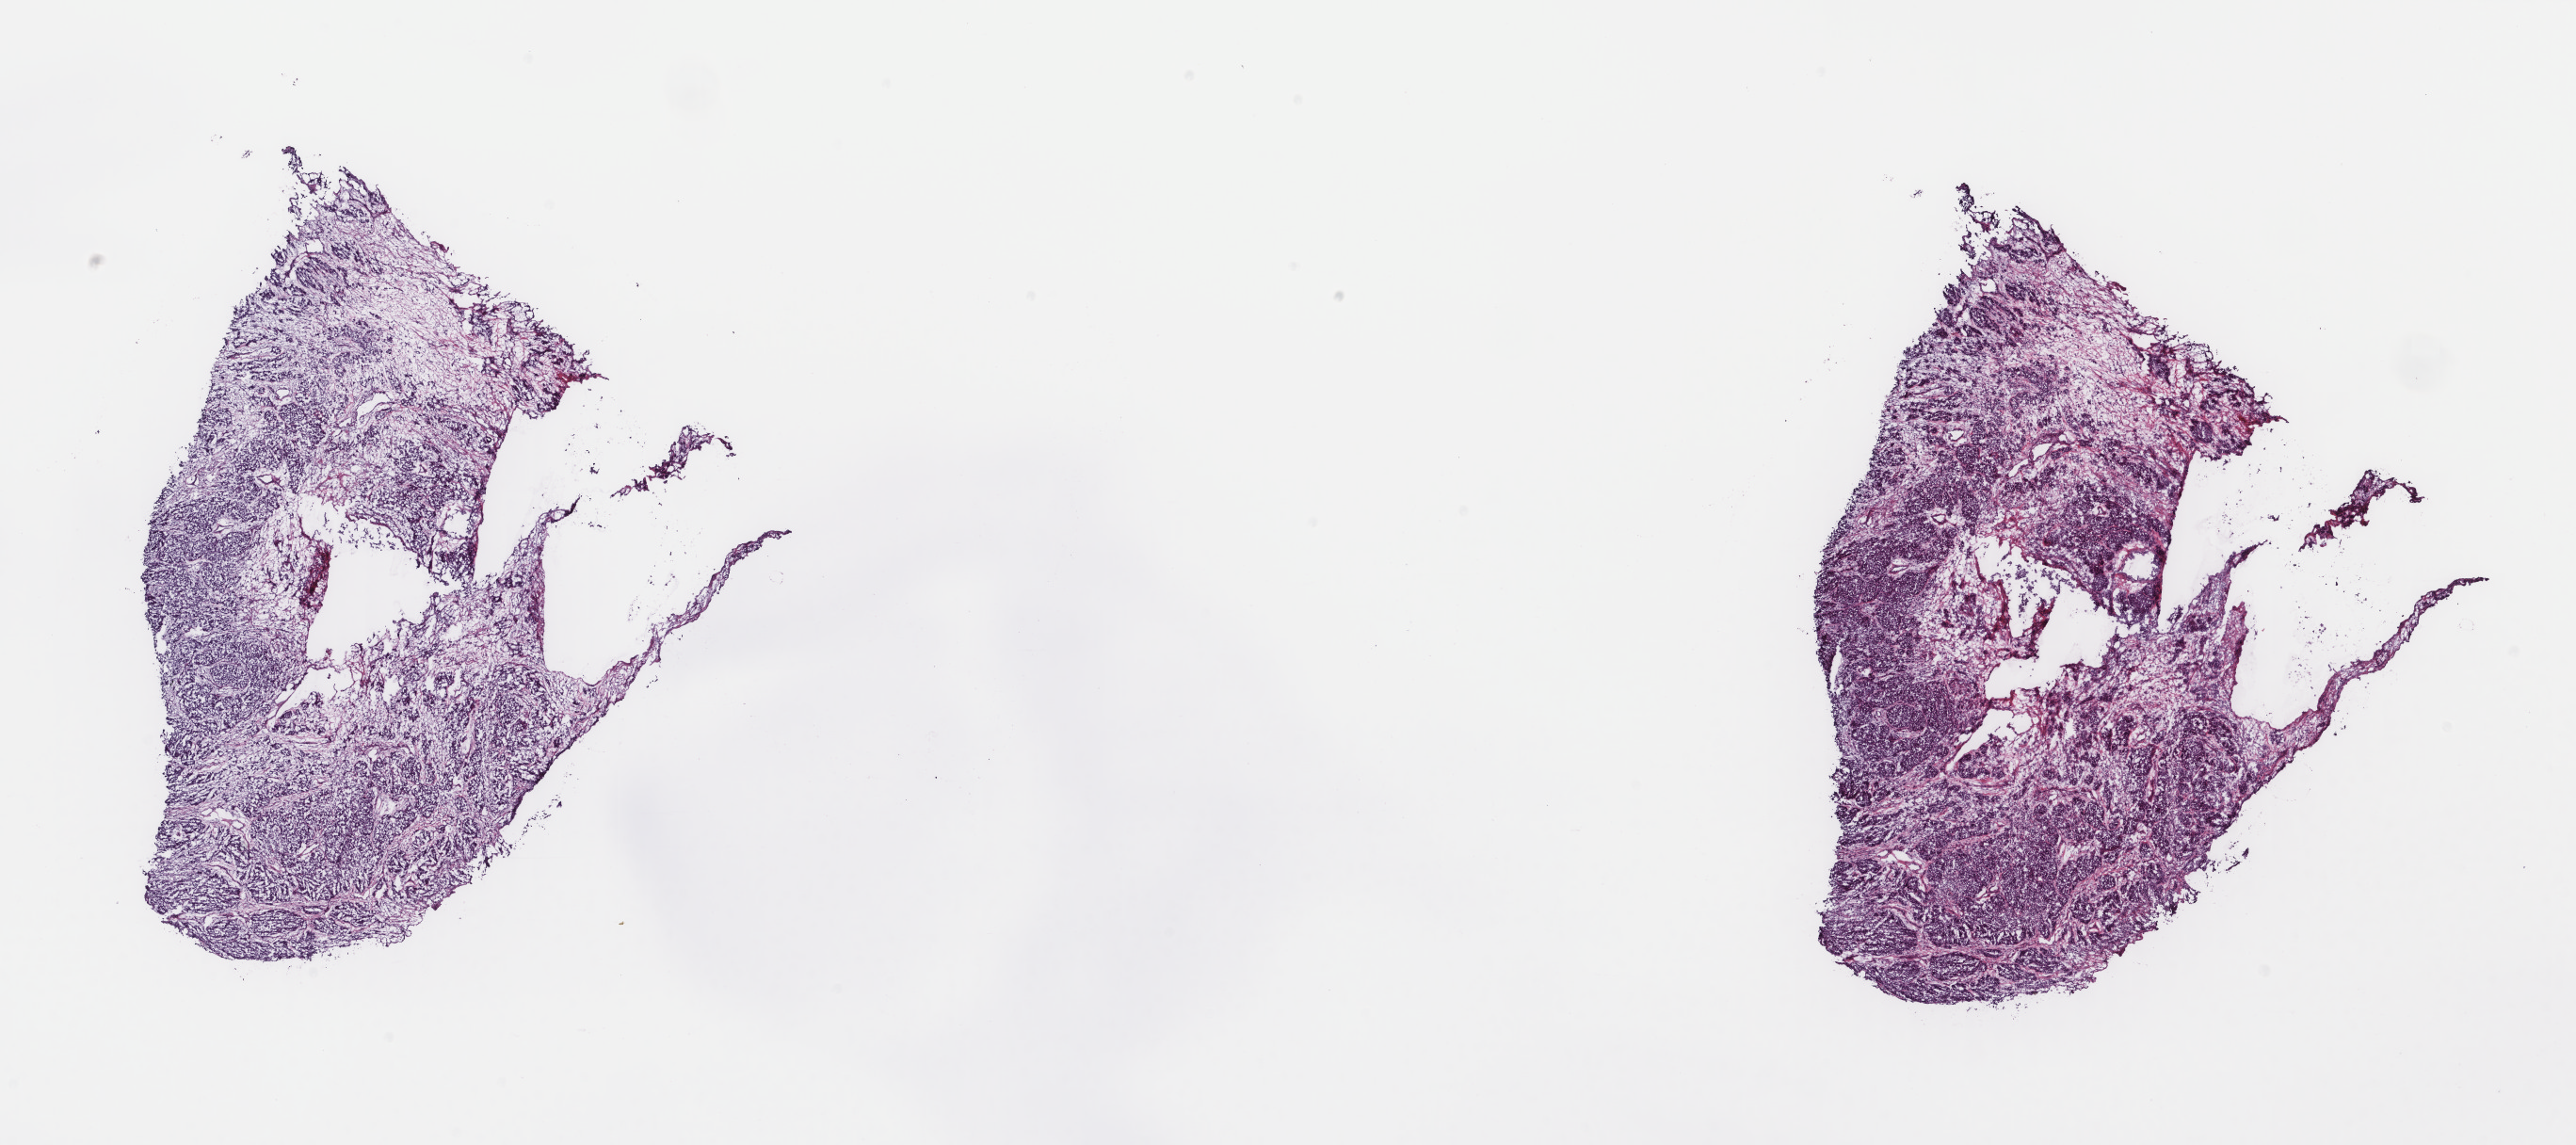
Whole-slide histology image, Hematoxylin and eosin (H&E) stained, a low-resolution overview of the entire scanned area, about 21.7 x 9.7 mm; frozen section from the top of the tissue portion; metastatic tumour sample, sampled site not recorded. Male, age 45 years at initial diagnosis. Composition of this section per pathologist review: tumour cells 80%, tumour nuclei 80%, normal cells 0%, stromal cells 20%, necrosis 0%. Infiltration values recorded for this section: lymphocyte infiltration 5%, monocyte infiltration 0%, neutrophil infiltration 0%.
This section: metastatic tumour tissue. Patient diagnosis: Malignant melanoma, NOS.